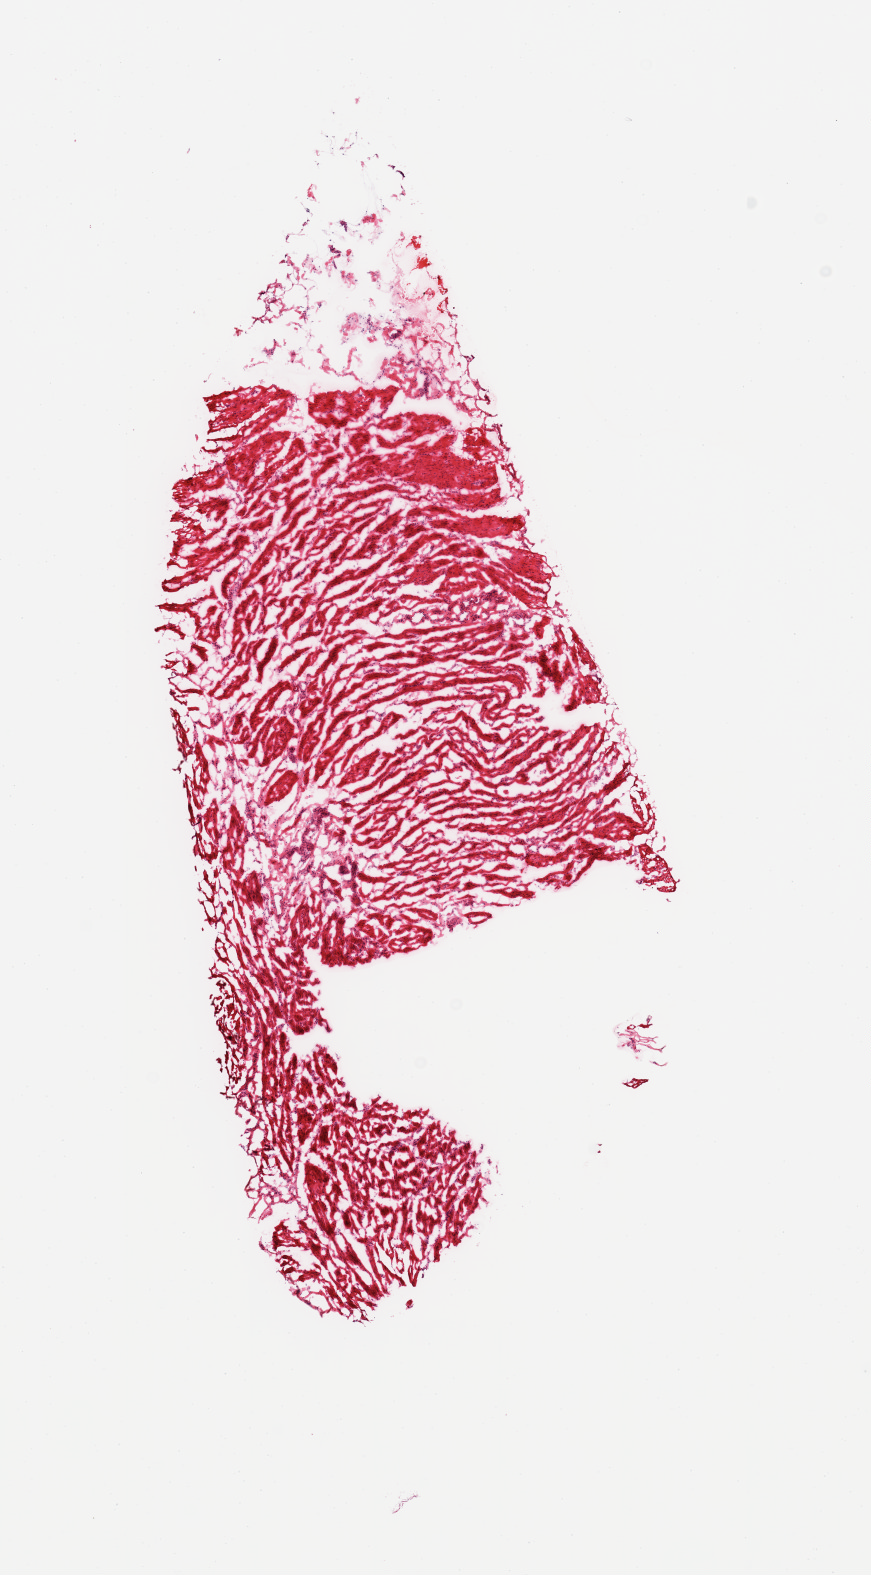
Hematoxylin and eosin (H&E) whole-slide image, shown as a low-resolution overview of the whole scanned area (about 6.9 x 12.5 mm, acquisition: 20x scan). Frozen section. Target tissue: esophageal muscle. Donor tissue sample. Donor: female.
Reviewer comment on this tissue sample: 1 piece; 20% fatty stroma at 1 edge.